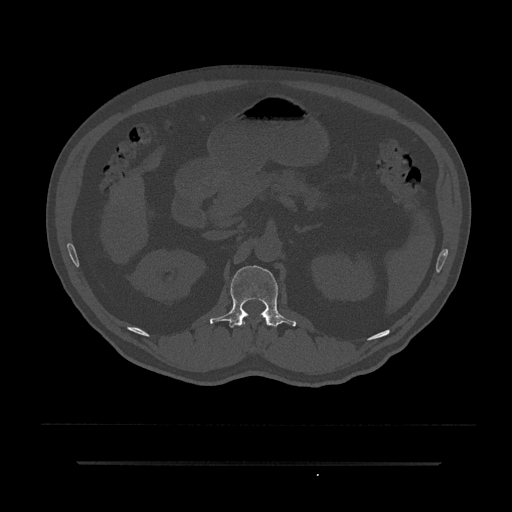
CT including the spine, one axial slice; position 156 of 797 along the scan axis; reconstruction kernel Br40s/3; 120 kVp; bone window (W 1800 / L 400 HU); 512 × 512 image matrix, field of view 464 × 464 mm. Patient: male, 59 years. Case-level facts recorded for this patient, not image findings: primary cancer: bile ducts; vertebrae with lytic lesions (as recorded): T10.
Outlined on this slice (semi-automatically segmented with operator editing):
- L1 vertebra: box from (x=210, y=265) to (x=296, y=327) px
- T12 vertebra: (x=242, y=321)–(x=268, y=327)